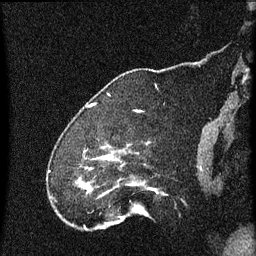
Breast MRI (dynamic contrast-enhanced), one sagittal slice; slice 14 of 60 in the series (ordered by position); dynamic contrast-enhanced series, image 2 of 4 at this slice position (ordered by acquisition); 1.5 T; TE 4.2 ms, TR 8 ms; 2 mm slice thickness; 256 × 256 image matrix, field of view 180 × 180 mm. Patient: female, 52 years.
Structures marked on this image (semi-automatically segmented with operator editing):
- analysis volume of interest (the breast-tissue region the enhancement analysis was run in; not a lesion): bounding box [x1, y1, x2, y2] px = [75, 150, 155, 219]
- tumour enhancement mask (voxels above the 70 % enhancement threshold inside the analysis volume of interest): [80, 158, 126, 219]